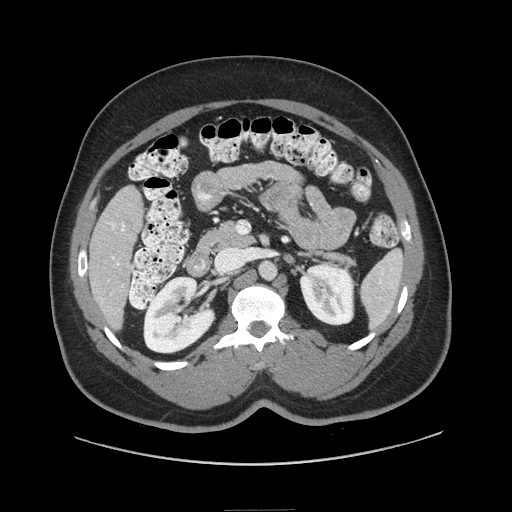
Contrast-enhanced abdominal CT (liver protocol), one axial slice; slice 28 of 87 in the series (ordered by position); reconstruction kernel STANDARD; soft-tissue window (W 400 / L 40 HU); 2.5 mm slice thickness; 512 × 512 image matrix. Case-level facts recorded for this patient, not image findings: diagnosis: hepatocellular carcinoma (patient treated with transarterial chemoembolisation; whether this scan precedes or follows treatment is not stated here); TNM stage (as recorded): Stage-II; Child-Pugh class: A.
Structures marked on this image (semi-automatic segmentation, software-assisted and operator-edited):
- liver parenchyma outside the tumour (the mass and vessels are separate outlines, so this box may not span the whole liver): bounding box <88,186,142,328> (left, top, right, bottom; pixels)
- liver vessels: <108,222,125,287>